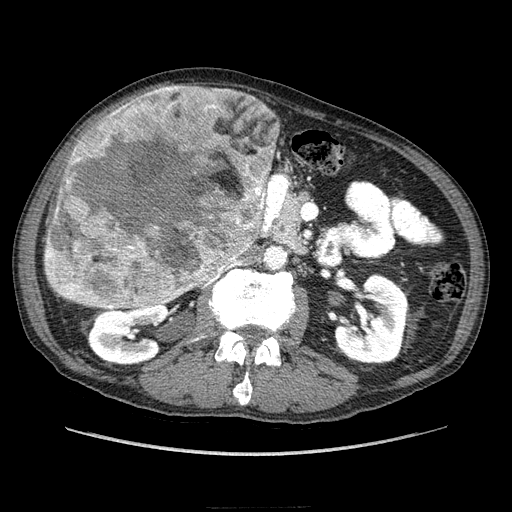
Contrast-enhanced abdominal CT (liver protocol), one axial slice. Position 99 of 218 along the scan axis. Soft-tissue window (W 400 / L 40 HU). 2.5 mm slice thickness. 512 × 512 image matrix, field of view 380 × 380 mm. Case-level facts recorded for this patient, not image findings: diagnosis: hepatocellular carcinoma (patient treated with transarterial chemoembolisation; whether this scan precedes or follows treatment is not stated here); TNM stage (as recorded): Stage-IIIA; Child-Pugh class: A; tumour differentiation: well differentiated; tumour nodularity: multinodular.
Outlined on this slice (semi-automatic segmentation, software-assisted and operator-edited):
- liver parenchyma outside the tumour (the mass and vessels are separate outlines, so this box may not span the whole liver): bounding box (x1, y1, x2, y2) in pixels: (66, 90, 254, 272)
- mass: (41, 85, 276, 312)
- liver vessels: (228, 261, 240, 268)